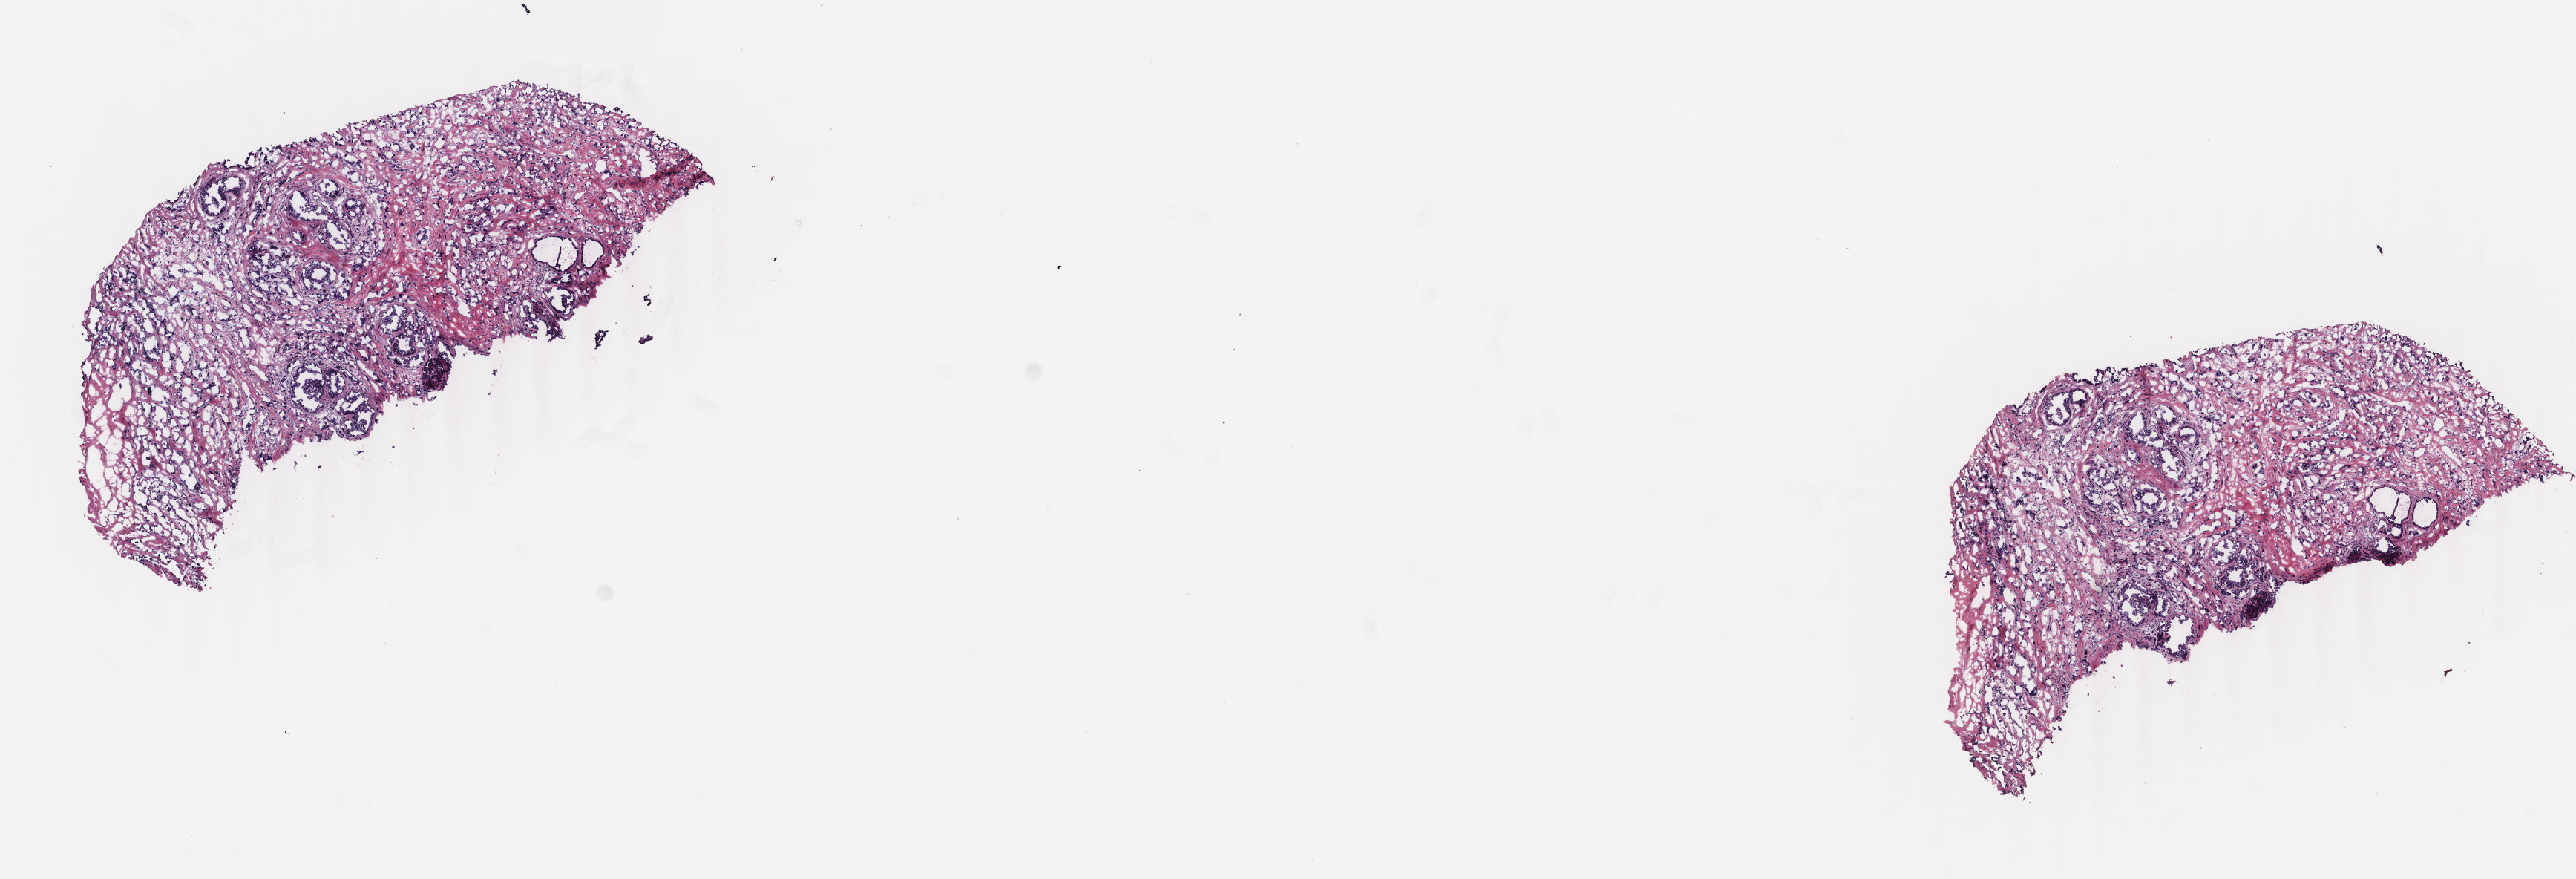
Whole-slide histology image, H&E, whole scanned area (about 13.8 x 4.7 mm, from a 40x scan) shown as a low-resolution overview; frozen section; primary tumour sample from the breast. Female patient; age at initial diagnosis 40 years. Pathologist review of this section (percent, as recorded): tumour cells 70%, tumour nuclei 70%, normal cells 0%, stromal cells 30%, necrosis 0%. Infiltration values recorded for this section: lymphocyte infiltration 2%, monocyte infiltration 1%, neutrophil infiltration 1%.
Histologic diagnosis: Infiltrating duct carcinoma, NOS. AJCC pathologic stage: IIIA (4th edition).